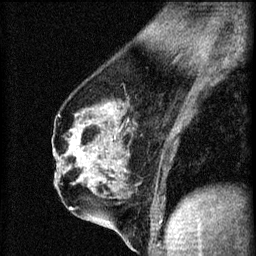
Breast MRI (dynamic contrast-enhanced), one sagittal slice; 3 images stored at this slice position (order not interpretable as contrast timing); 1.5 T; TE 4.2 ms, TR 8.2 ms; 2 mm slice thickness; 256 × 256 image matrix, field of view 180 × 180 mm. Female patient, age 56 years.
Structures marked on this image (semi-automatically segmented with operator editing):
- analysis volume of interest (the breast-tissue region the enhancement analysis was run in; not a lesion): bounding box (x1, y1, x2, y2) in pixels: (62, 136, 111, 179)
- tumour enhancement mask (voxels above the 70 % enhancement threshold inside the analysis volume of interest): (72, 142, 77, 145)